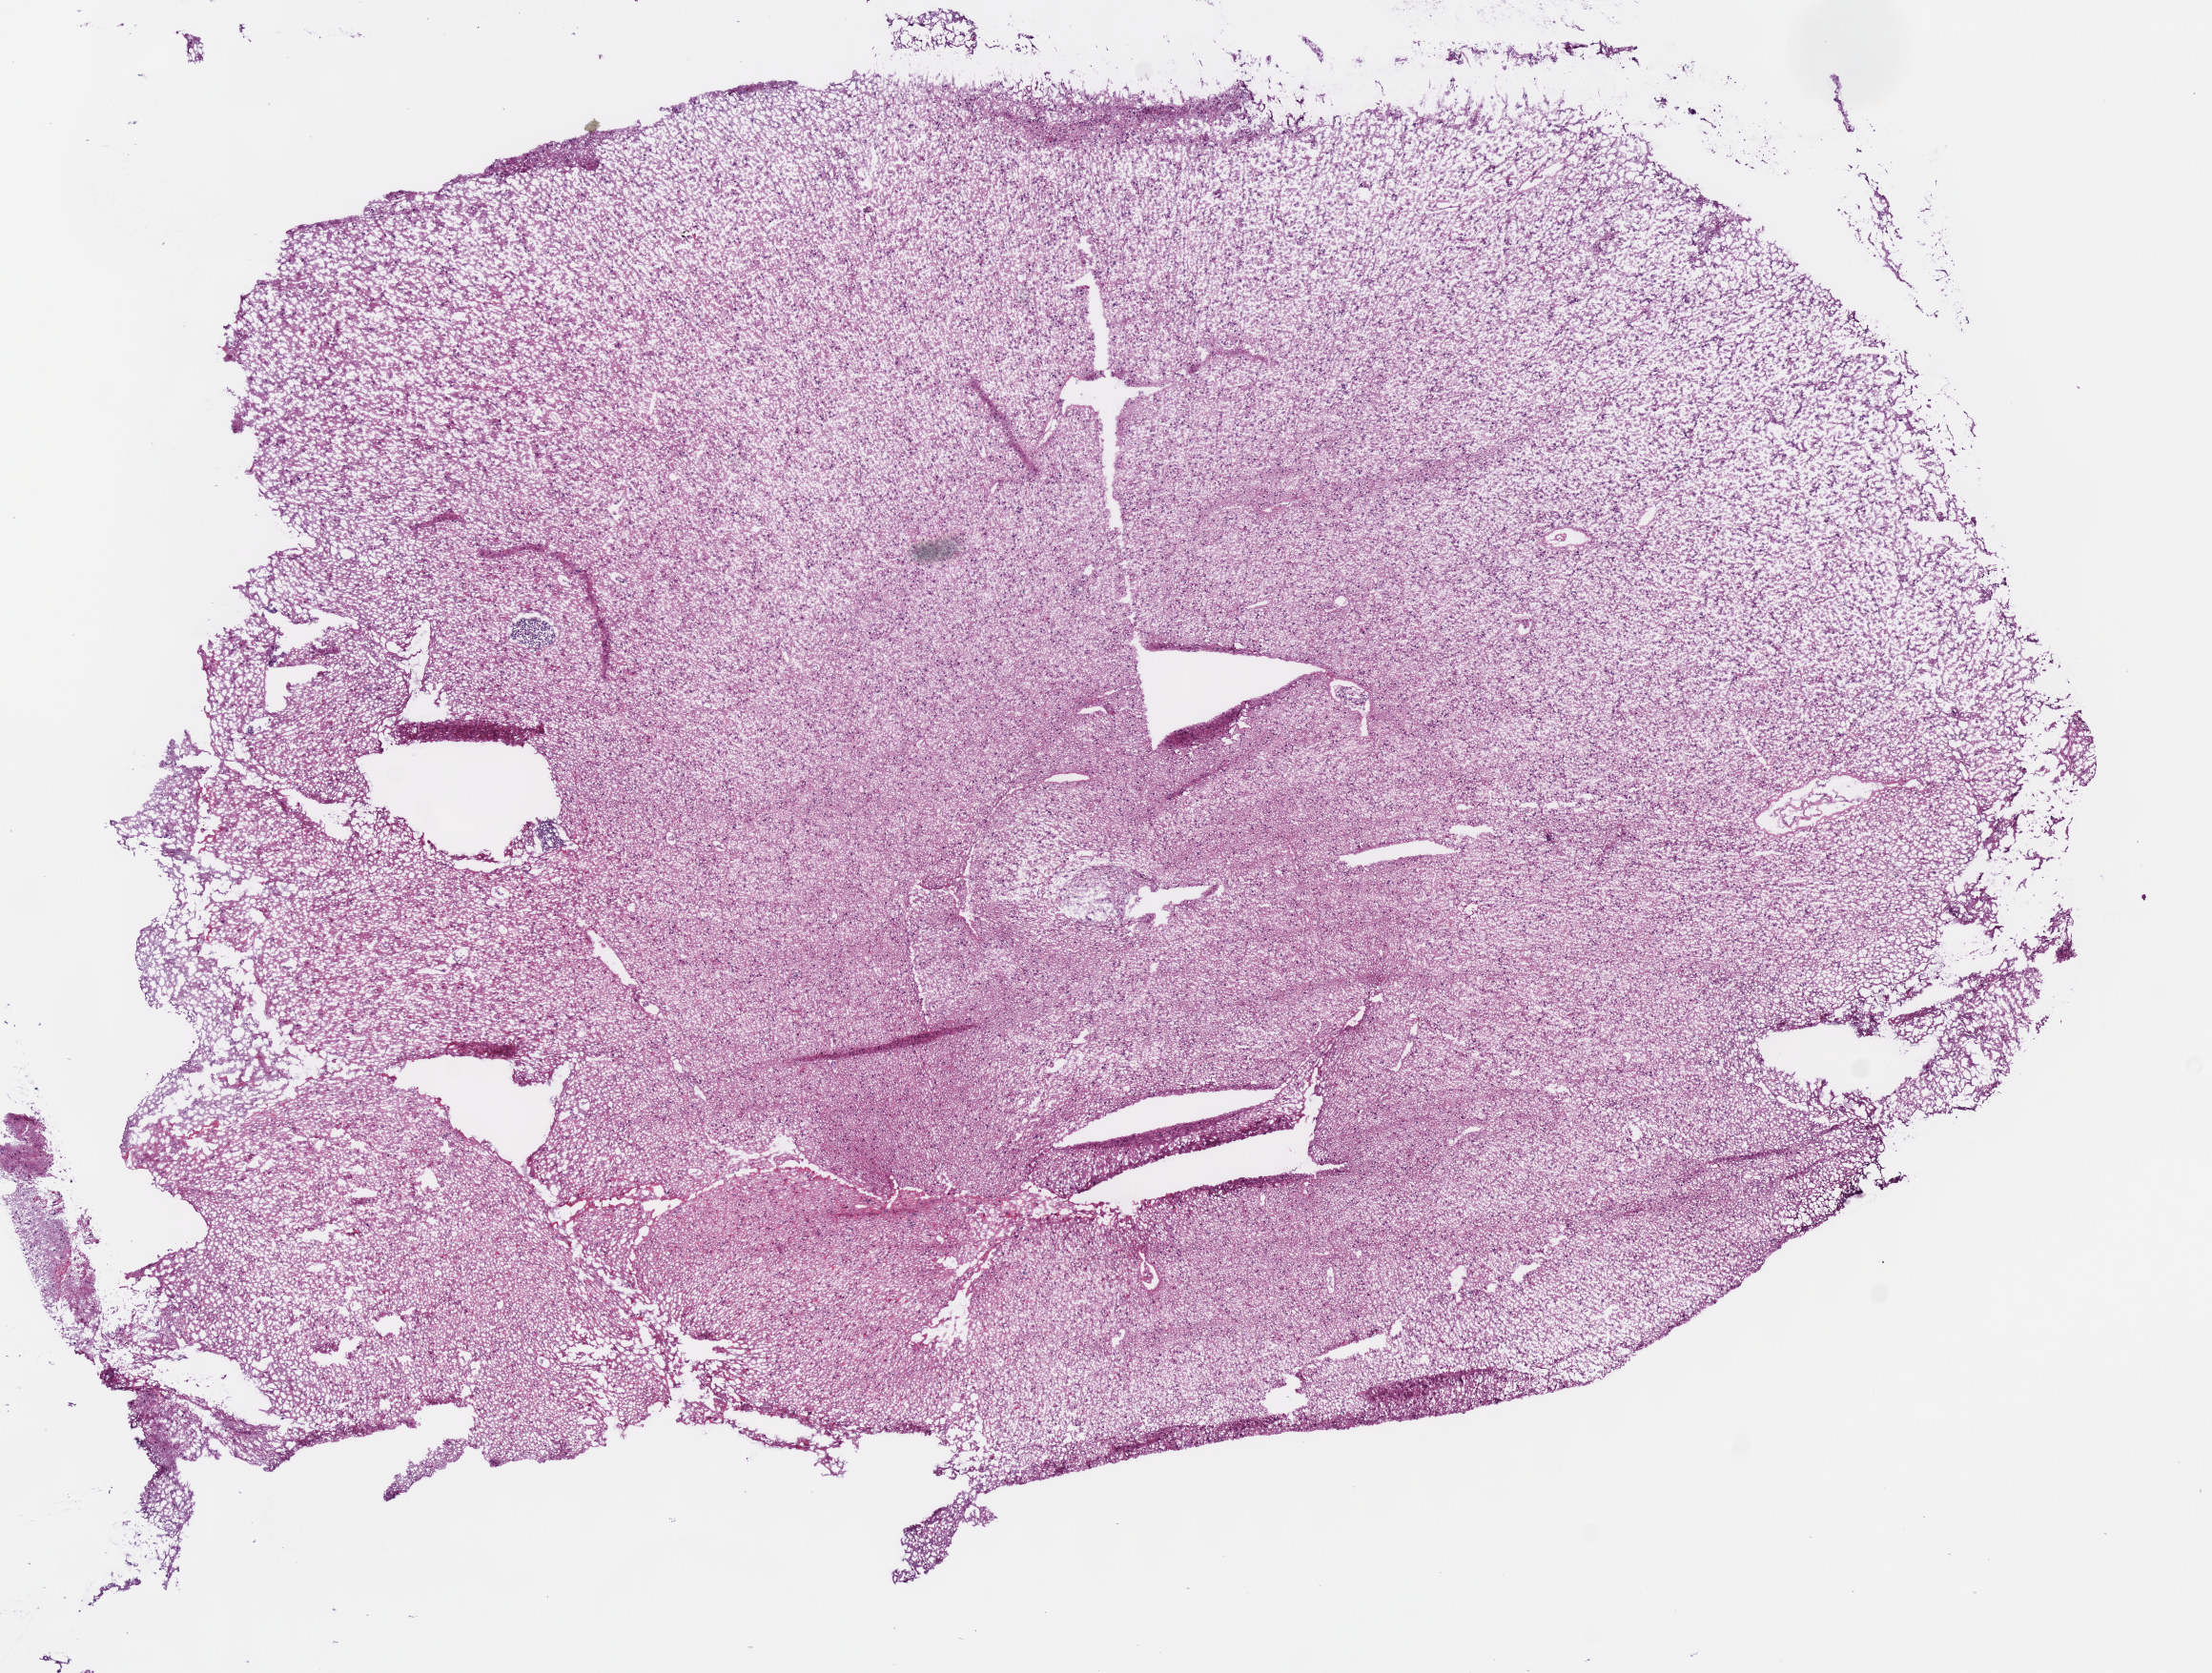
Whole-slide histology image, H&E-stained, low-resolution overview of the scanned area, about 9.1 x 6.9 mm. Frozen section from the bottom of the tissue portion. Sample: primary tumour, brain. Male, age 38 years at initial diagnosis.
Pathologic diagnosis: Oligodendroglioma, NOS (cerebrum).